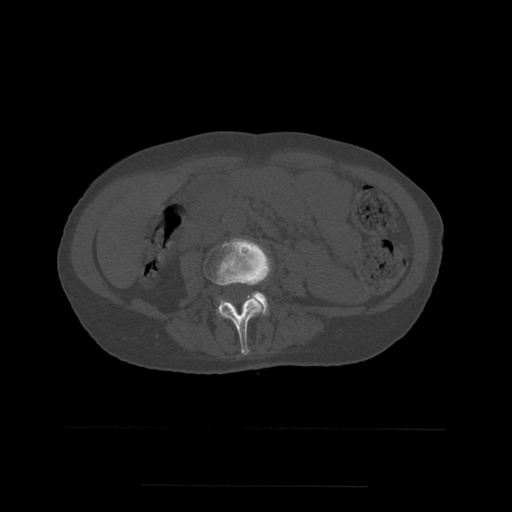
CT including the spine, one axial slice; position 182 of 544 along the scan axis; bone window (W 1800 / L 400 HU); 512 × 512 image matrix, field of view 350 × 350 mm. Patient age 58 years. Case-level facts recorded for this patient, not image findings: primary cancer: lung.
Annotated regions visible in this slice (semi-automatic segmentation, software-assisted and operator-edited):
- L3 vertebra: box from (x=203, y=238) to (x=272, y=355) px
- L4 vertebra: (x=218, y=292)–(x=269, y=316)